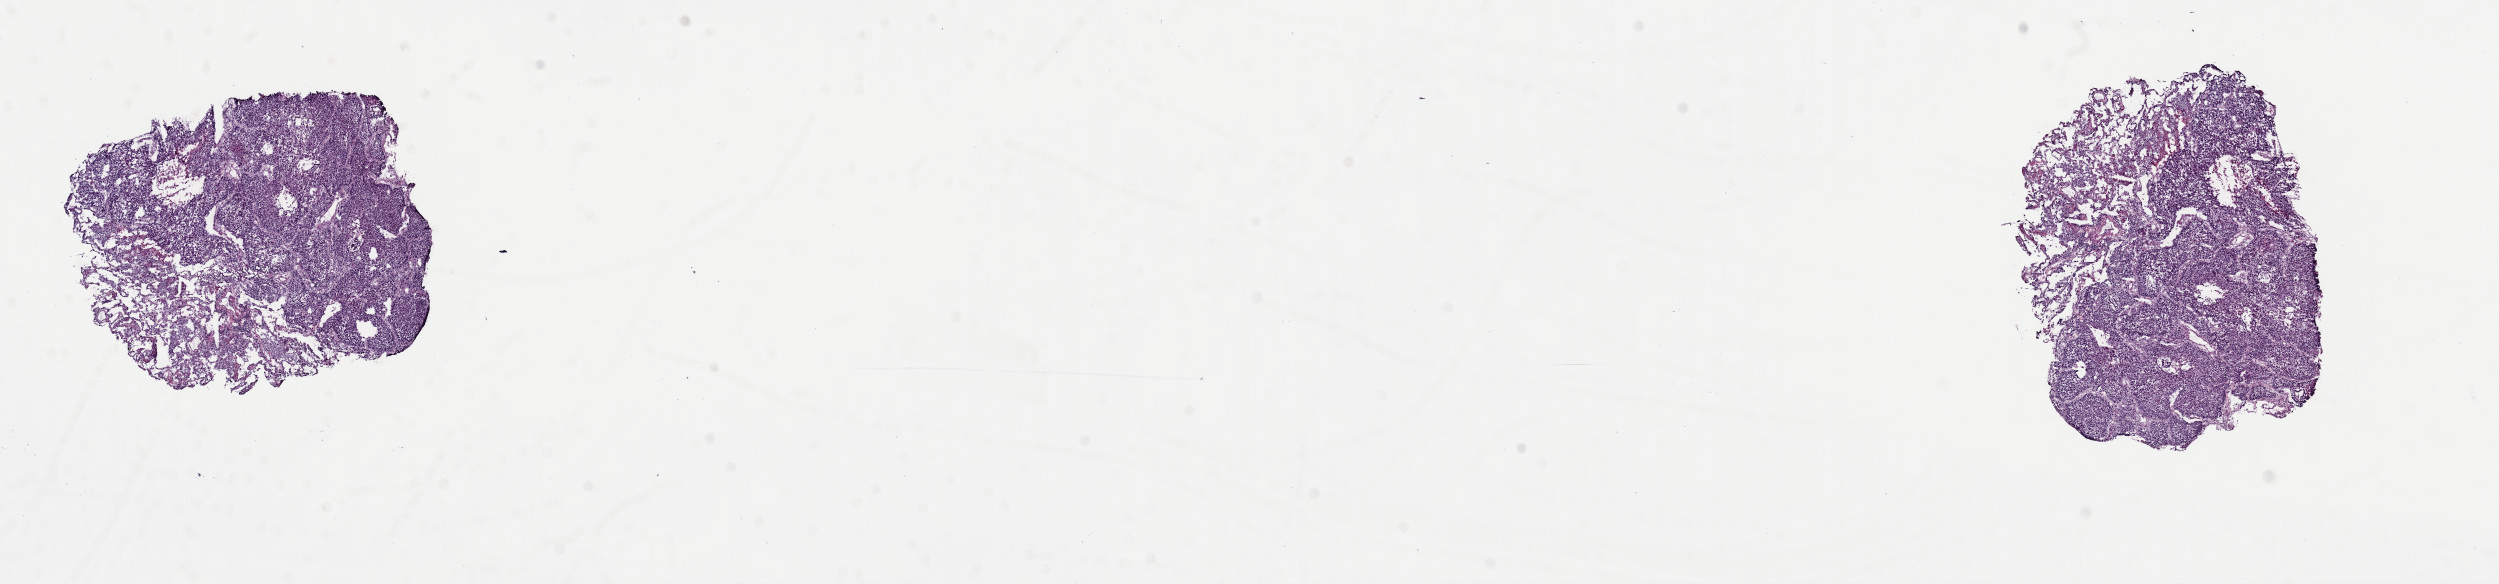
Whole-slide histology image, Hematoxylin and eosin (H&E) stained — a low-resolution overview of the entire scanned area, about 19.7 x 4.6 mm (acquisition: 40x scan); frozen section; primary tumour sample from the lung. Patient: male, age at initial diagnosis 62 years. Composition of this section per pathologist review: tumour cells 85%, tumour nuclei 90%, normal cells 5%, stromal cells 0%, necrosis 10%. Inflammatory infiltration, as recorded: lymphocyte infiltration 0%, monocyte infiltration 0%, neutrophil infiltration 0%.
AJCC pathologic stage: IB (6th edition). Histologic diagnosis: Squamous cell carcinoma, NOS.